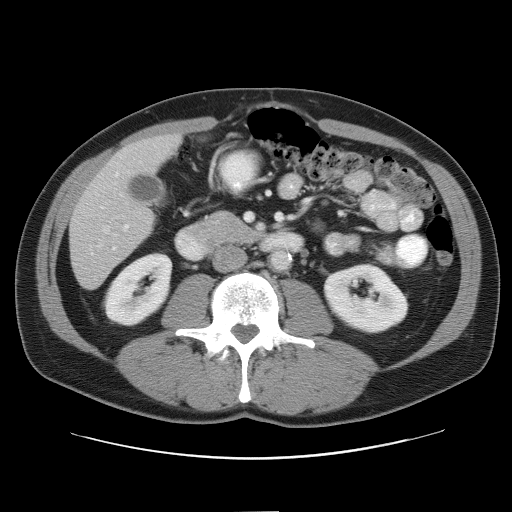
Contrast-enhanced abdominal CT, one axial slice; slice 21 of 52 in the series (ordered by position); intravenous contrast given; soft-tissue window (W 400 / L 40 HU); 512 × 512 image matrix. Male patient, age 70 years. From the clinical record (not read from this slice): diagnosis: colorectal cancer liver metastases, imaged before liver resection.
Structures marked on this image (outlined manually by an expert reader):
- hepatic veins: bounding box <89,225,117,255> (left, top, right, bottom; pixels)
- liver: <71,135,180,288>
- planned liver remnant (the part of the liver to remain after resection): <118,135,179,175>
- portal vein (with intrahepatic branches): <114,163,129,230>